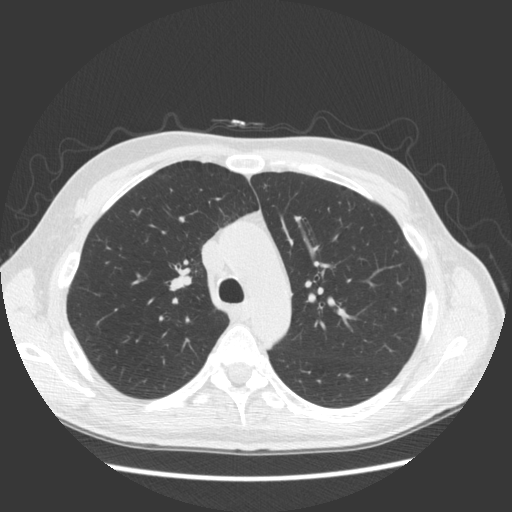
Low-dose screening chest CT, axial slice, second annual screen, lung window (W 1500 / L -600 HU), 2.5 mm slice thickness, standard (soft-tissue) reconstruction kernel (STANDARD), slice 54 of 163 in the series. Male participant, aged 57 years at enrolment. Former smoker at enrolment.
• Lesion marked by an expert reader, bounding box (x1, y1, x2, y2) in pixels: (152, 247, 204, 301).
• The screening reader recorded 3 non-calcified nodules or masses ≥4 mm on this exam (right middle lobe, right middle lobe, right middle lobe); which of them this box marks is not recorded.
• Official screen result: negative screen, minor abnormalities not suspicious for lung cancer.
• Later outcome: lung cancer diagnosed 264 days after this screen — adenocarcinoma, NOS, right upper lobe, poorly differentiated (G3), stage IB (AJCC 6th edition), 25 mm at pathology.